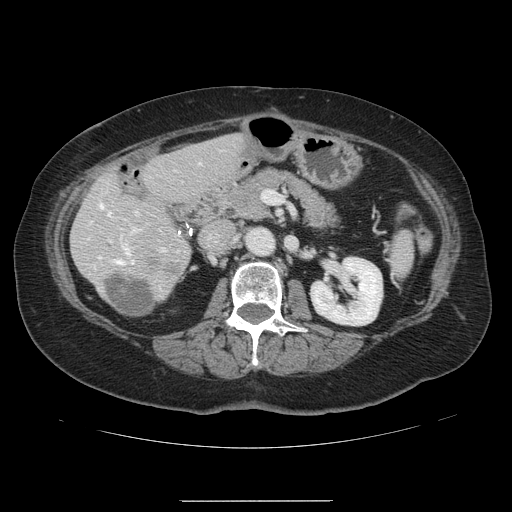
Contrast-enhanced abdominal CT, one axial slice; position 54 of 141 along the scan axis; intravenous contrast given; soft-tissue window (W 400 / L 40 HU); 2.5 mm slice thickness; 512 × 512 image matrix, field of view 393 × 393 mm. Female patient, age 74 years. From the clinical record (not read from this slice): diagnosis: colorectal cancer liver metastases, imaged before liver resection; multiple liver metastases: yes; largest metastasis: 7 cm; disease in both lobes: yes.
Annotated regions visible in this slice (outlined manually by an expert reader):
- hepatic veins: box from (x=100, y=204) to (x=134, y=264) px
- liver: (x=72, y=135)–(x=245, y=317)
- planned liver remnant (the part of the liver to remain after resection): (x=86, y=135)–(x=245, y=317)
- portal vein (with intrahepatic branches): (x=109, y=162)–(x=201, y=251)
- liver metastasis: (x=109, y=276)–(x=158, y=315)
- liver metastasis: (x=146, y=258)–(x=186, y=281)